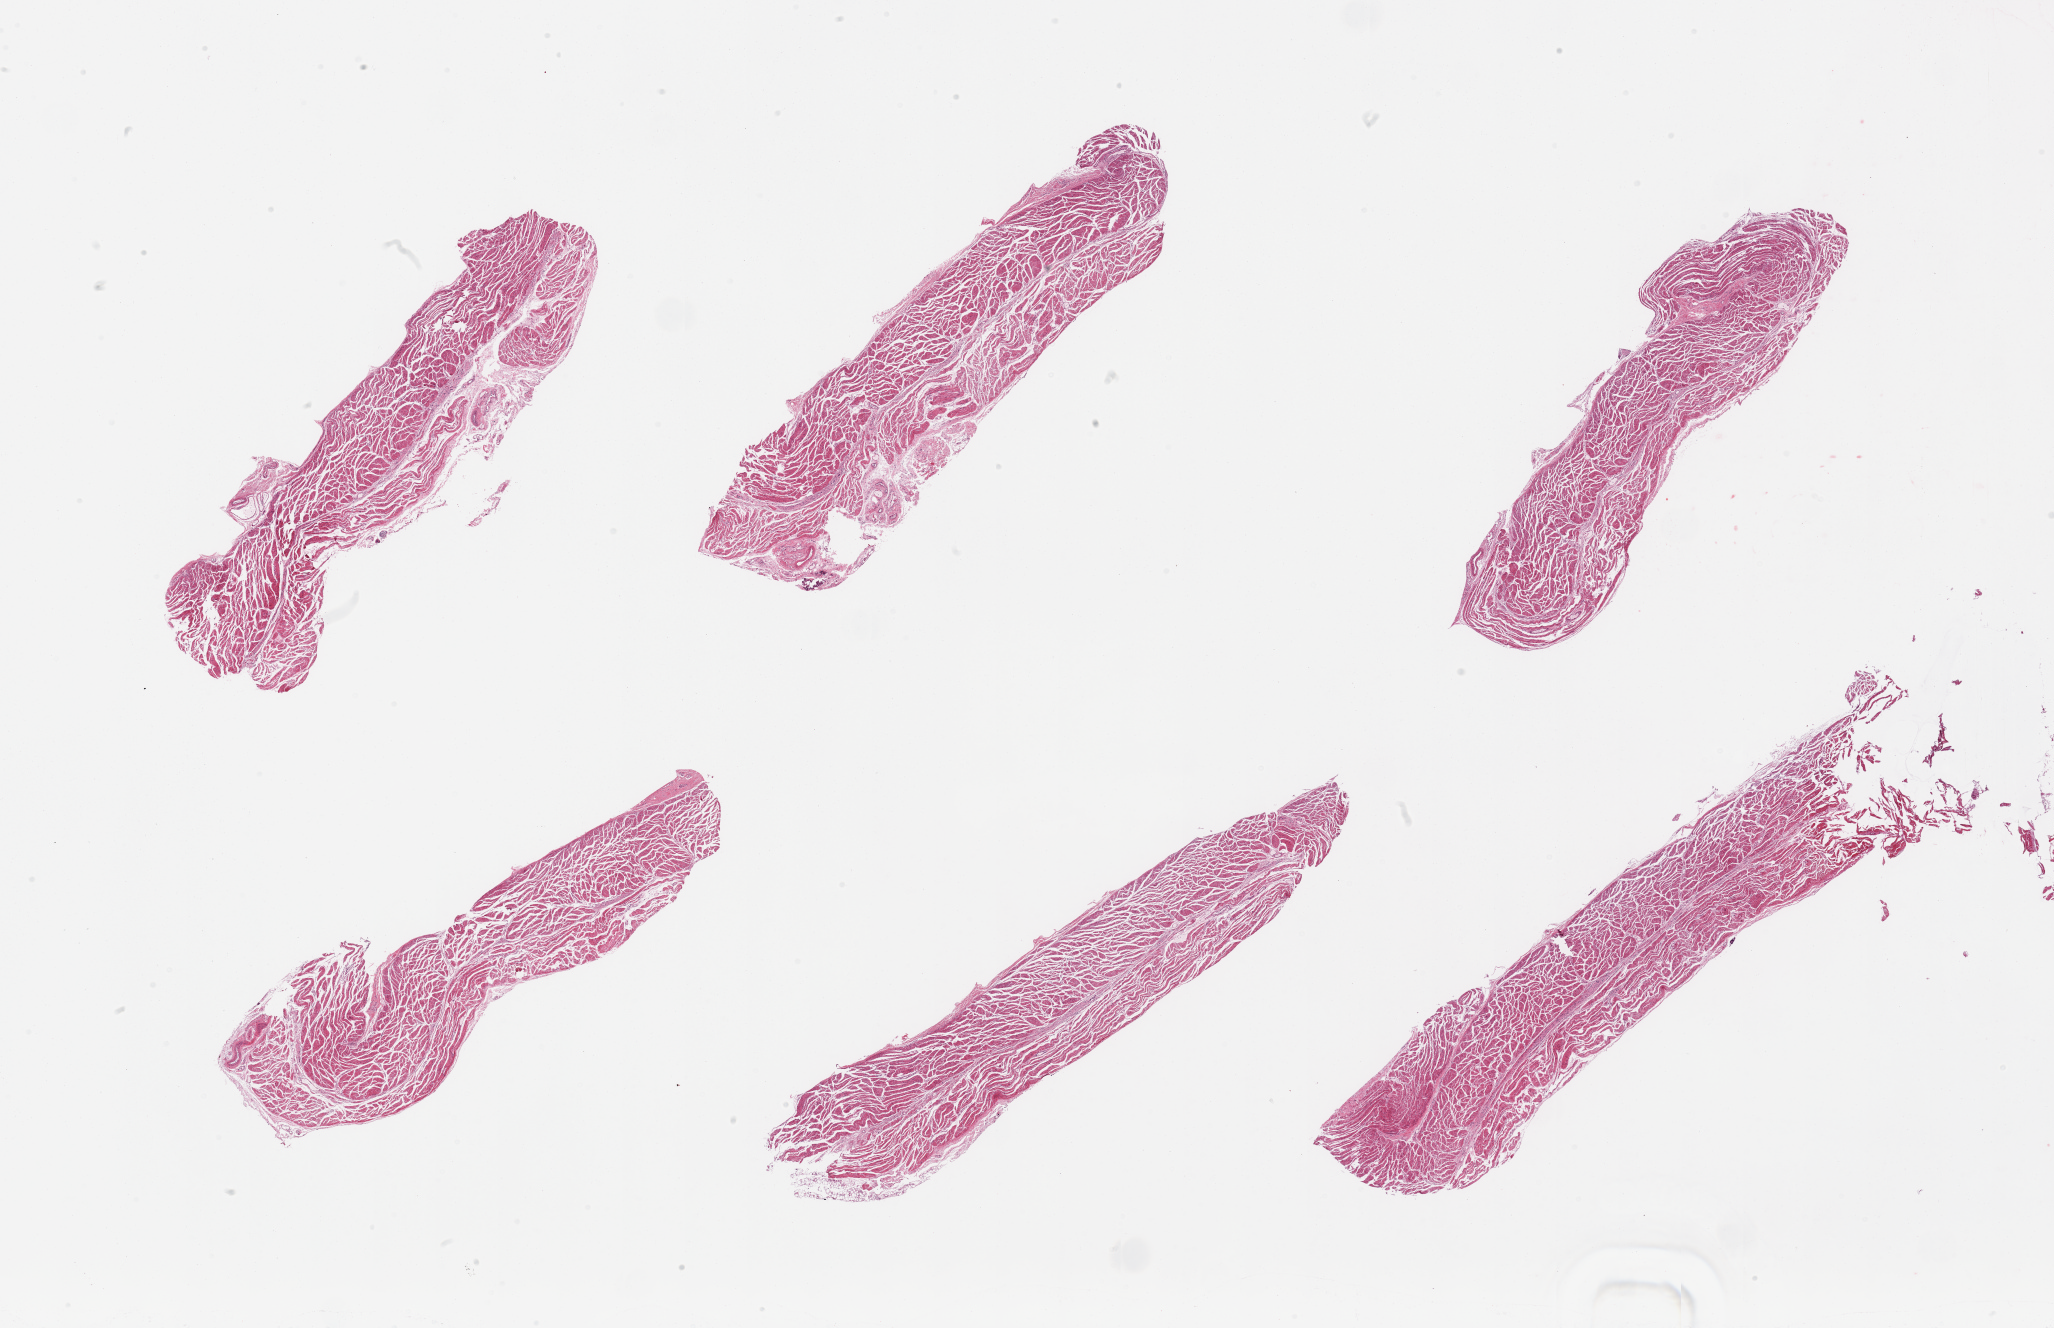
H&E whole-slide image, a low-resolution overview of the entire scanned area, about 32.5 x 21.0 mm, PAXgene-fixed, paraffin-embedded tissue, target tissue: esophageal muscle, tissue donor sample. Male donor.
Pathologist's review note for this sample: 6 pieces, target muscularis, good specimen.